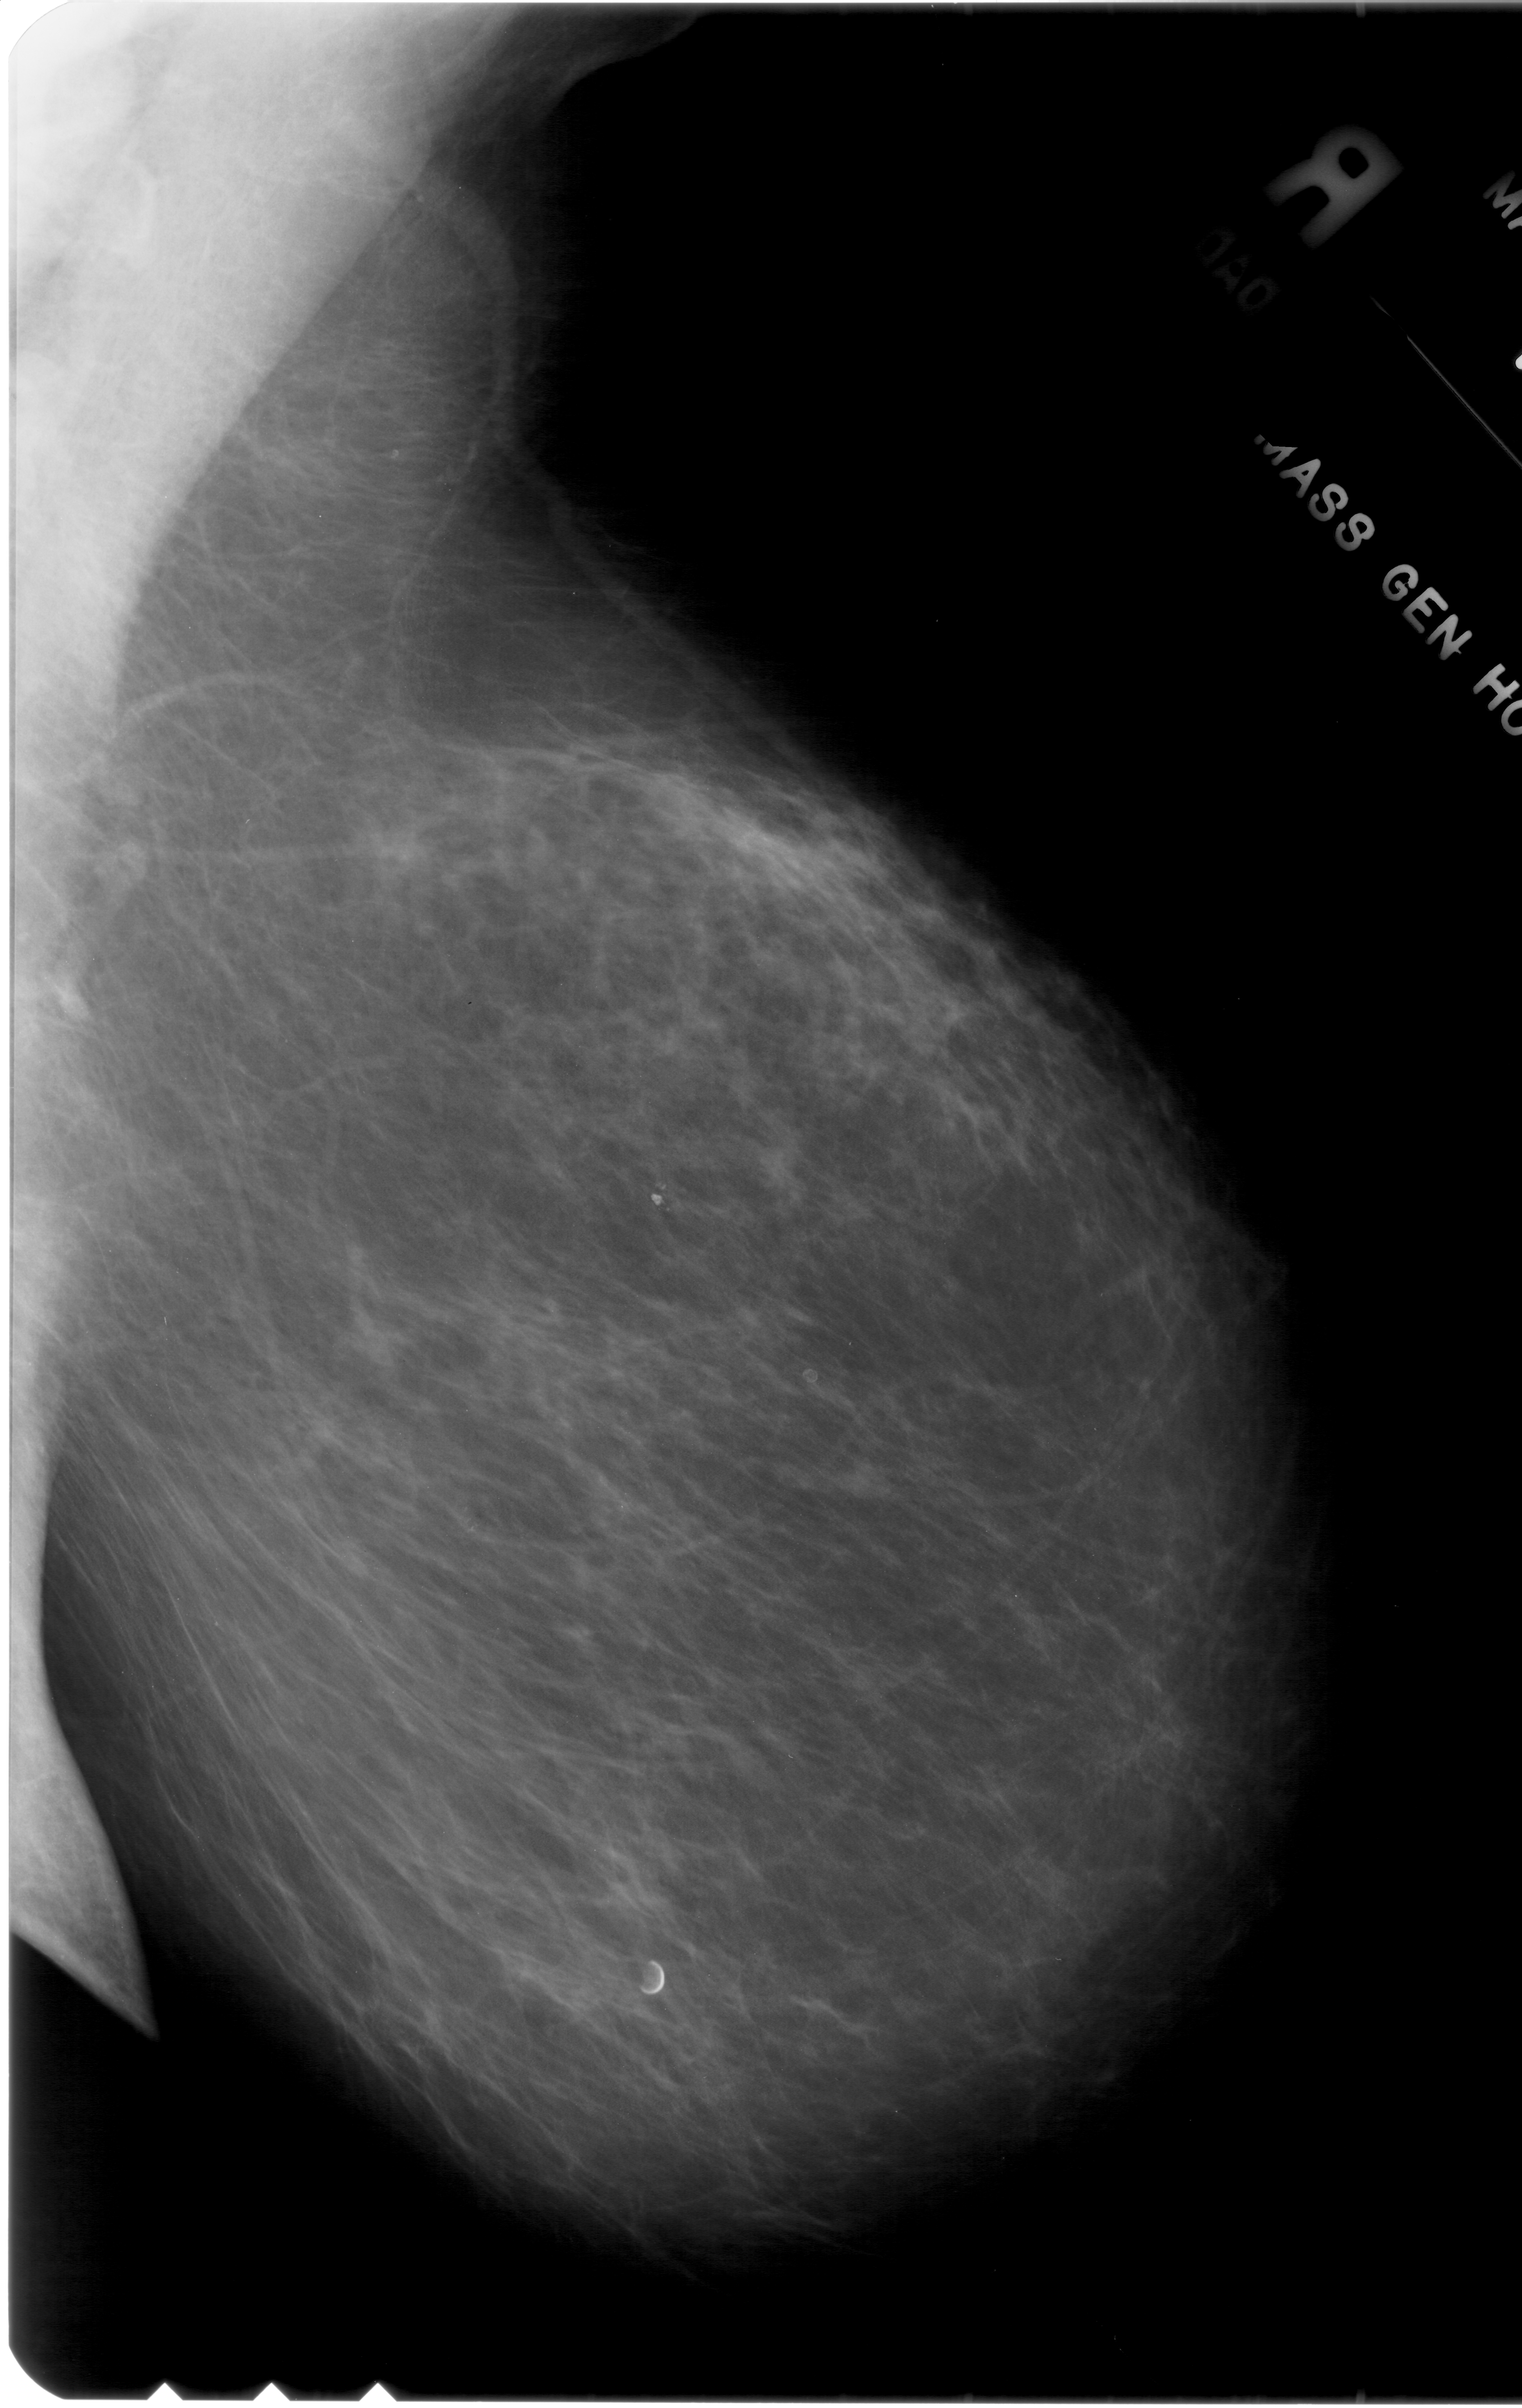
Digitized screen-film mammogram, right breast, mediolateral oblique (MLO) view.
Radiologist-marked abnormalities on this image: calcifications, morphology pleomorphic, distribution clustered; BI-RADS assessment category 4; pathology result (as recorded, not read from the image): benign.